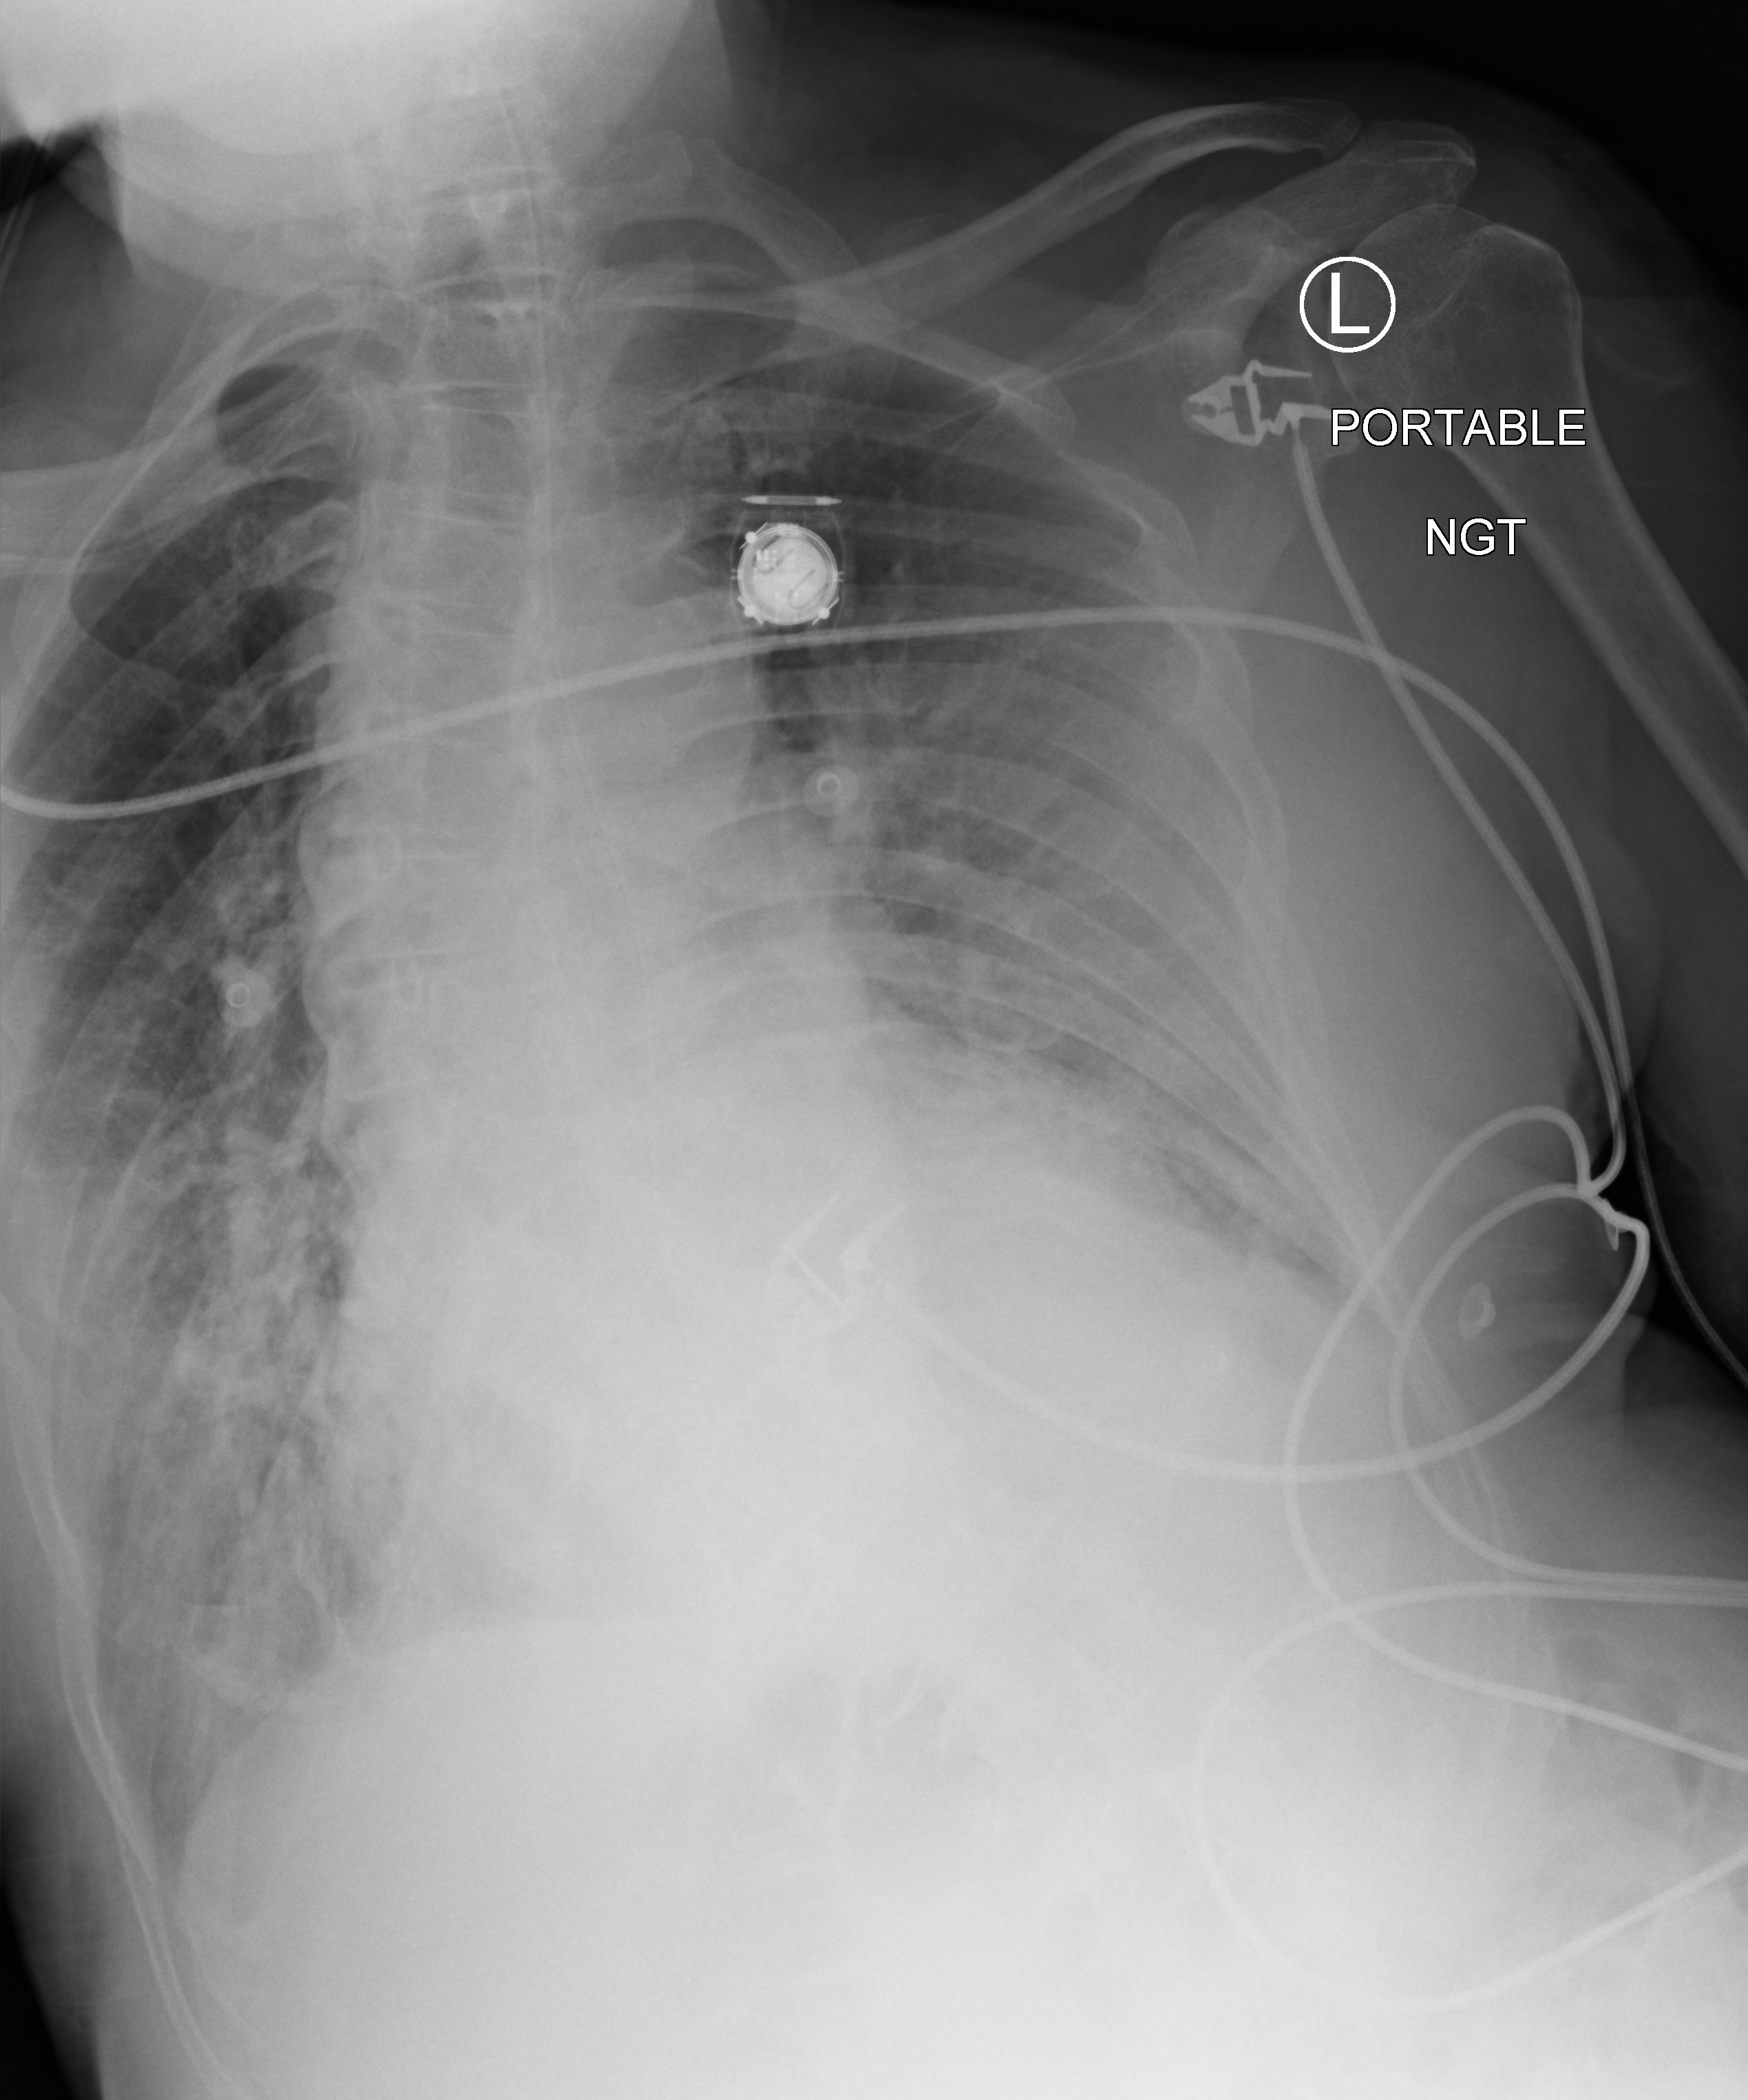
Portable chest radiograph; anteroposterior (AP) projection. Patient hospitalised with COVID-19; male, aged 75–90 years.
From the hospital-stay record, not from the radiograph (when in the stay this image was taken is not recorded): mechanically ventilated during this hospital stay: no; admitted to intensive care during this hospital stay: no.